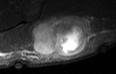
MRI of an extremity soft-tissue mass, one axial slice. Slice 20 of 36 in the series (ordered by position). STIR. MR volume resampled by the dataset authors to the PET/CT grid (not the native acquisition matrix). 3.27 mm slice thickness. 116 × 74 image matrix, field of view 113 × 72 mm. Male patient. Case-level facts recorded for this patient, not image findings: histological type: pleiomorphic leiomyosarcoma; grade: high; site of the primary tumour: left buttock.
Annotated regions visible in this slice (expert contour drawn on MRI and transferred to this co-registered scan by the dataset authors):
- gross tumour volume including surrounding oedema: bounding box <28,16,86,57> (left, top, right, bottom; pixels)
- gross tumour volume (mass): <28,19,83,57>